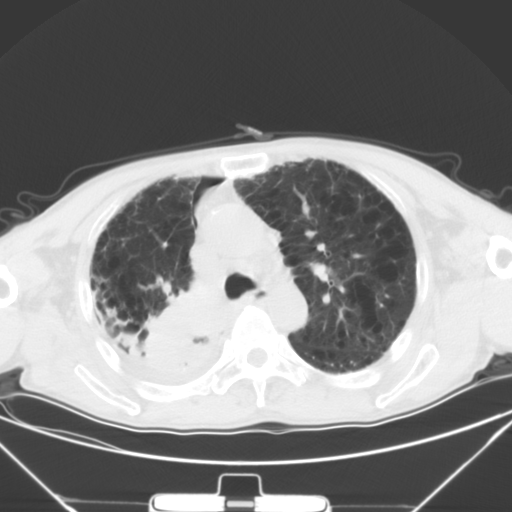
Chest CT, one axial slice. Slice 33 of 50 in the series (ordered by position). 120 kVp. Lung window (W 1500 / L -600 HU). 5 mm slice thickness. 512 × 512 image matrix, field of view 373 × 373 mm. Male patient, age 65 years. Case-level facts recorded for this patient, not image findings: clinical TNM (as recorded): T3 N1 M1a.
Annotated regions visible in this slice (rectangle marked by the reading radiologist):
- lung tumour (recorded histology: squamous cell carcinoma): box from (x=137, y=283) to (x=225, y=383) px